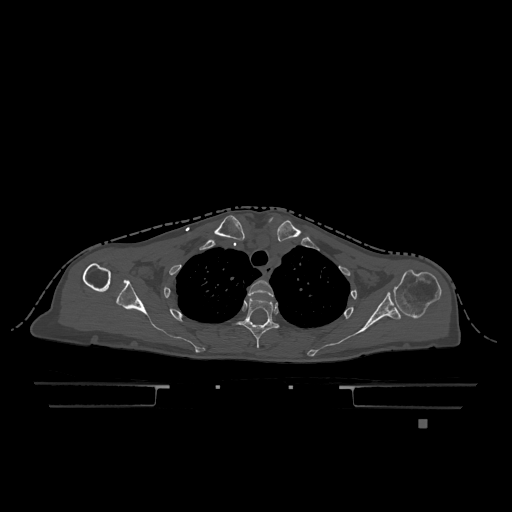
CT including the spine, one axial slice. Bone window (W 1800 / L 400 HU). 0.5 mm slice thickness. 512 × 512 image matrix, field of view 500 × 500 mm. Female patient, age 74 years. From the clinical record (not read from this slice): primary cancer: lung; vertebrae with lytic lesions (as recorded): T1, T4, T5, T6, L4, L5.
Outlined on this slice (semi-automatically segmented with operator editing):
- T2 vertebra: bounding box (x1, y1, x2, y2) in pixels: (248, 280, 274, 297)
- T3 vertebra: (235, 298, 279, 348)